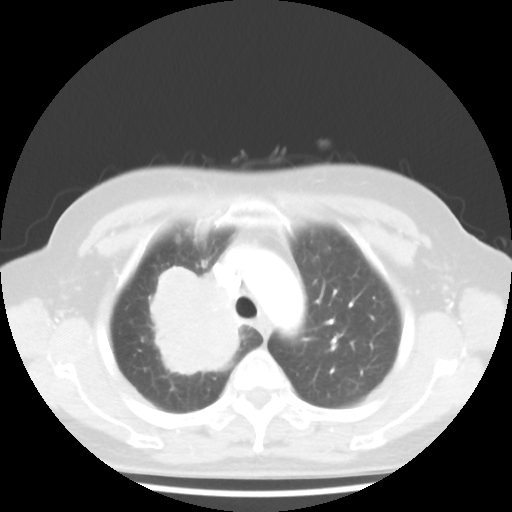
Chest CT, one axial slice; slice 34 of 44 in the series (ordered by position); 100 kVp; lung window (W 1500 / L -600 HU); 5 mm slice thickness; 512 × 512 image matrix, field of view 316 × 316 mm. Female patient, age 62 years. From the clinical record (not read from this slice): clinical TNM (as recorded): T3 N0 M0; histopathological grade: G3.
Structures marked on this image (rectangle marked by the reading radiologist):
- lung tumour (recorded histology: small cell carcinoma): bounding box (x1, y1, x2, y2) in pixels: (137, 256, 242, 391)